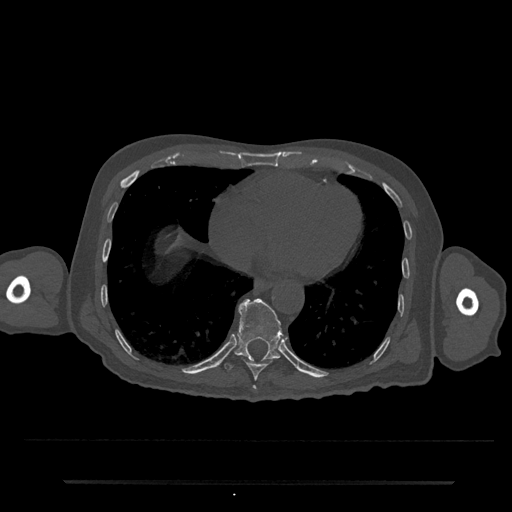
CT including the spine, one axial slice. Position 338 of 797 along the scan axis. 120 kVp. Bone window (W 1800 / L 400 HU). 512 × 512 image matrix, field of view 427 × 427 mm. Patient: male, 74 years. From the clinical record (not read from this slice): primary cancer: prostate.
Annotated regions visible in this slice (semi-automatically segmented with operator editing):
- T10 vertebra: box from (x=224, y=298) to (x=284, y=370) px
- T8 vertebra: (x=253, y=385)–(x=256, y=390)
- T9 vertebra: (x=243, y=359)–(x=273, y=381)